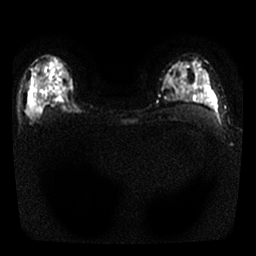
Breast MRI, one axial slice. Slice 18 of 25 in the series (ordered by position). Diffusion-weighted series; image 2 of 4 stored at this slice position (different b-values; order by instance number). 1.5 T. 4 mm slice thickness. 256 × 256 image matrix, field of view 300 × 300 mm. Female patient.
Annotated regions visible in this slice (expert manual segmentation):
- tumour on diffusion-weighted imaging: box from (x=27, y=66) to (x=79, y=115) px